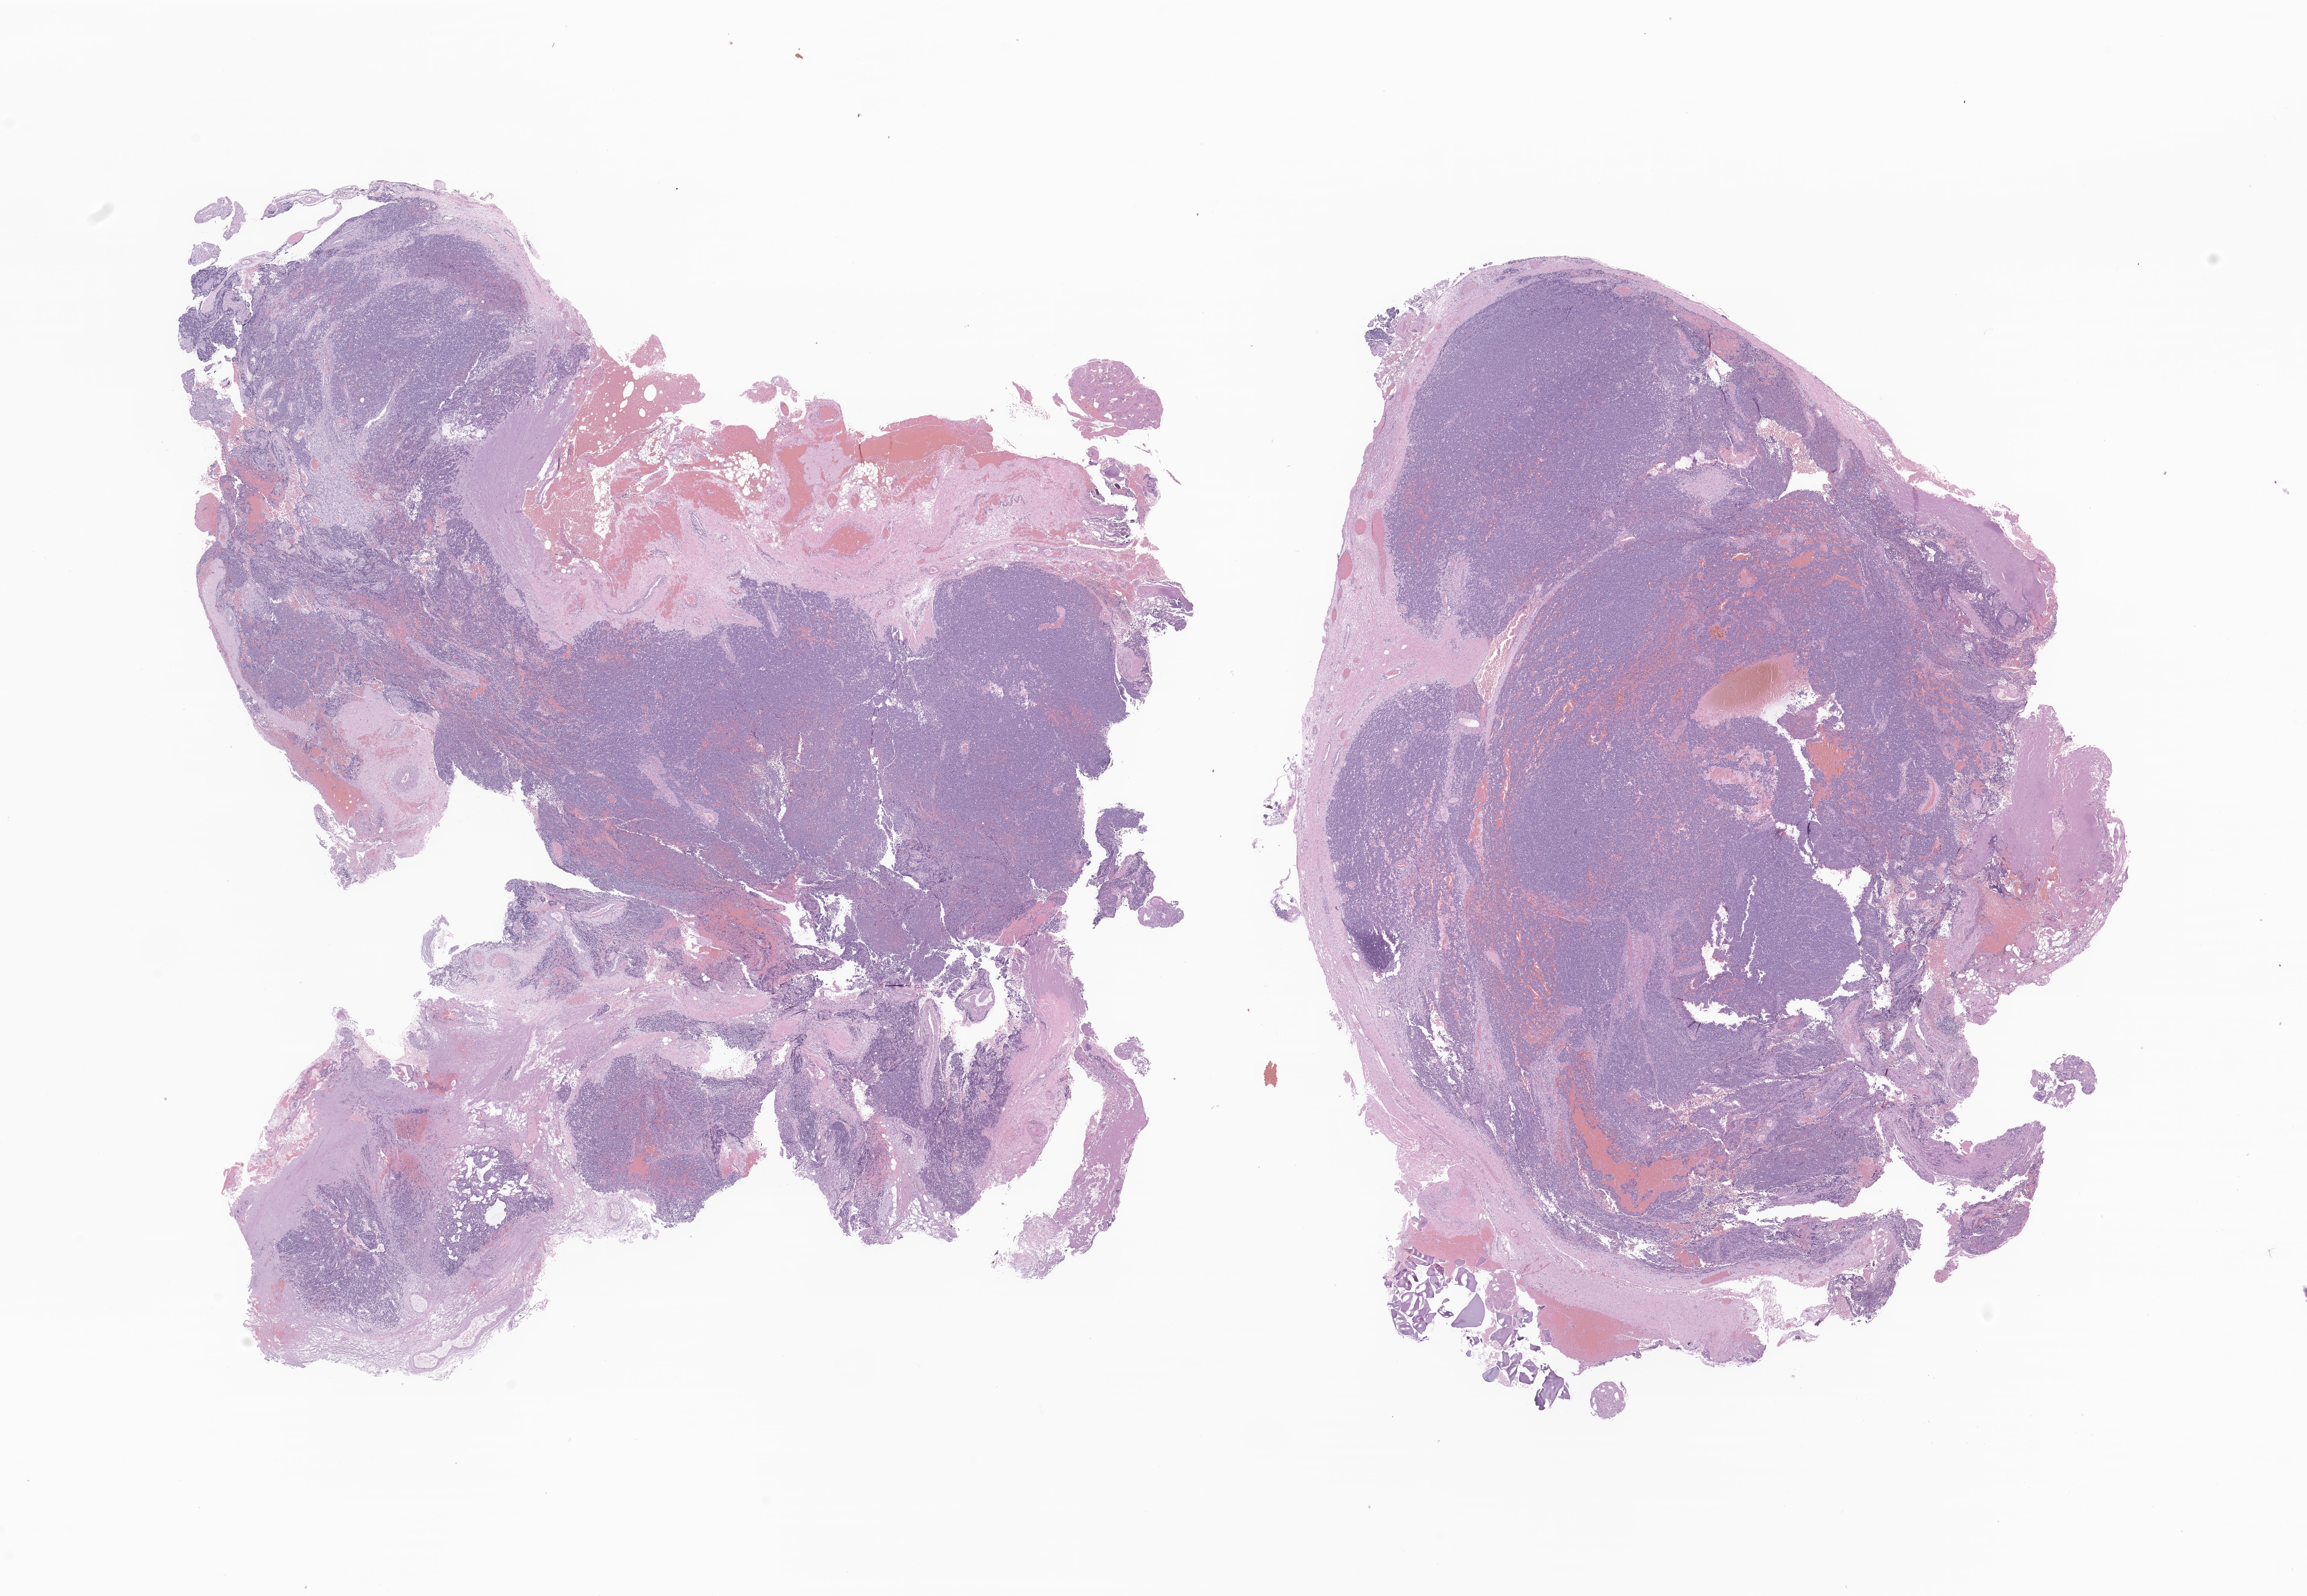
Digitized hematoxylin and eosin (H&E)-stained section of tumor tissue from the soft tissue of thorax — low-resolution overview of the scanned area, about 24.4 x 16.9 mm. Female patient, age 194 months.
Specimen: formalin-fixed, paraffin-embedded (FFPE) tissue.